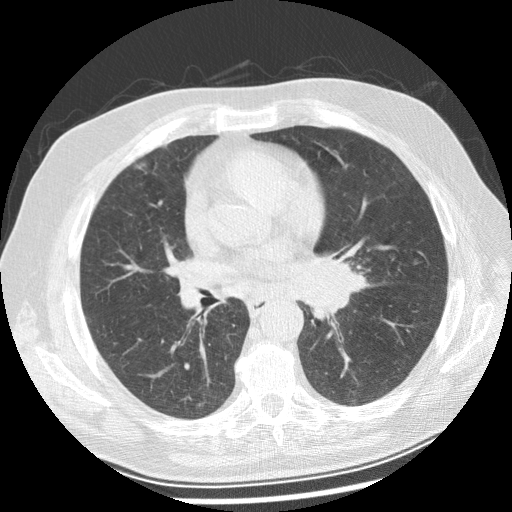
Low-dose screening chest CT, one axial slice. Slice 133 of 250 in the series (ordered by position). Reconstruction kernel STANDARD. 120 kVp. Lung window (W 1500 / L -600 HU). 2.5 mm slice thickness. 512 × 512 image matrix, field of view 360 × 360 mm.
Annotated regions visible in this slice (expert manual segmentation):
- lesion 1 (tumor, left main bronchus): bounding box [x1, y1, x2, y2] px = [301, 263, 370, 319]